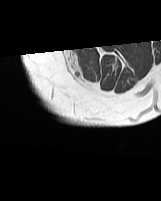
MRI of an extremity soft-tissue mass, one axial slice. Slice 6 of 70 in the series (ordered by position). MR volume resampled by the dataset authors to the PET/CT grid (not the native acquisition matrix). 3.27 mm slice thickness. 161 × 201 image matrix, field of view 157 × 196 mm. Female patient. Case-level facts recorded for this patient, not image findings: histological type: synovial sarcoma; grade: intermediate; site of the primary tumour: right buttock.
Structures marked on this image (expert contour drawn on MRI and transferred to this co-registered scan by the dataset authors):
- gross tumour volume including surrounding oedema: bounding box (x1, y1, x2, y2) in pixels: (63, 52, 82, 80)